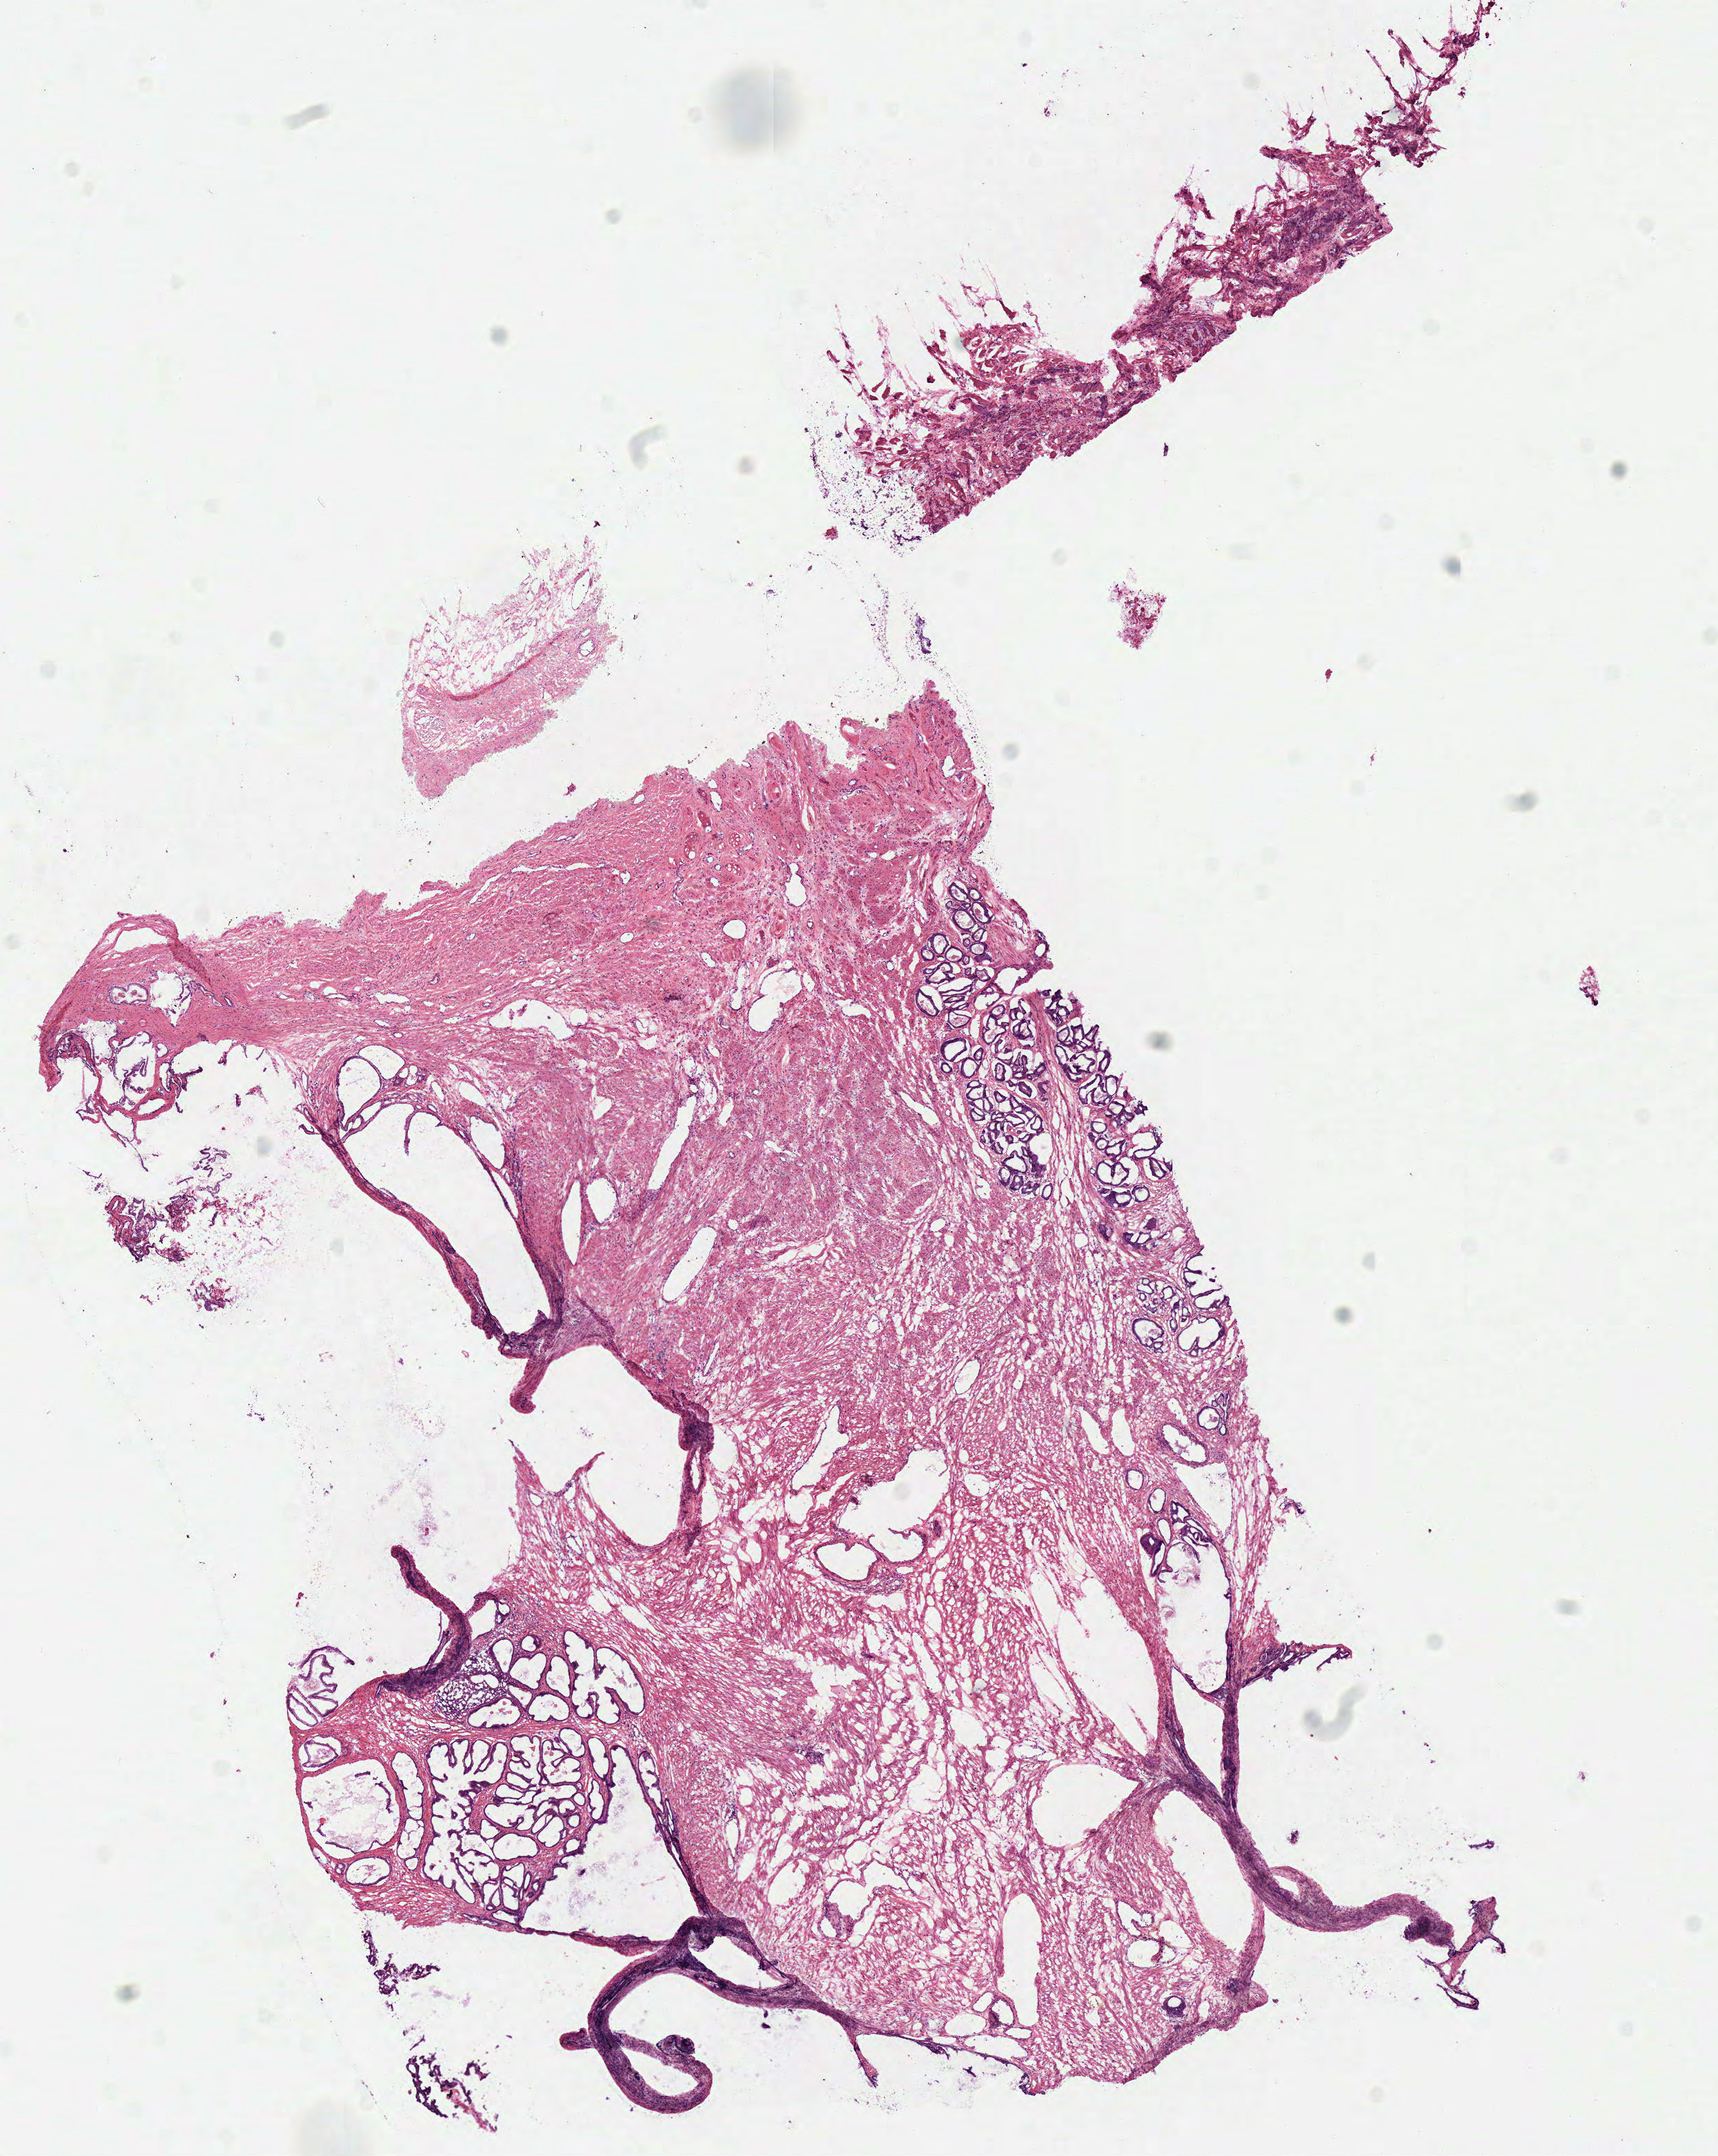
Hematoxylin and eosin (H&E) stained whole-slide image, whole scanned area (about 9.8 x 12.3 mm, from a 40x scan) shown as a low-resolution overview; frozen section from the top of the tissue portion; solid tissue normal (non-tumour tissue) sample from the prostate. Male patient; age at initial diagnosis 68 years.
* this section: solid tissue normal (non-tumour) sample from the same patient
* patient diagnosis: Acinar cell carcinoma (prostate gland)